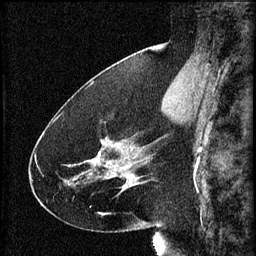
Breast MRI (dynamic contrast-enhanced), one sagittal slice; 3 images stored at this slice position (order not interpretable as contrast timing); 1.5 T; TE 4.2 ms, TR 8.2 ms; 256 × 256 image matrix, field of view 180 × 180 mm. Patient: female, 41 years.
Structures marked on this image (semi-automatically segmented with operator editing):
- analysis volume of interest (the breast-tissue region the enhancement analysis was run in; not a lesion): bounding box [x1, y1, x2, y2] px = [72, 122, 134, 195]
- tumour enhancement mask (voxels above the 70 % enhancement threshold inside the analysis volume of interest): [92, 144, 134, 187]